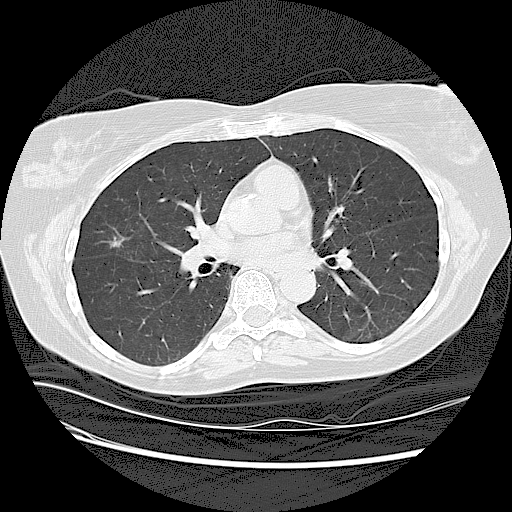
Low-dose screening chest CT, axial slice; first (baseline) screen; lung window (W 1500 / L -600 HU); slice 64 of 125 in the series. Female, age 63 years at enrolment. Current smoker at enrolment.
Lesion marked by an expert reader, bounding box <94,224,144,267> (left, top, right, bottom; pixels). Screening reader's record for this exam (one nodule recorded; not confirmed to be the boxed lesion): non-calcified nodule or mass ≥4 mm, right upper lobe, 7 × 7 mm, spiculated (stellate) margins, soft tissue attenuation. Official screen result: positive, change unspecified: nodule(s) >= 4 mm or enlarging nodule(s), mass(es), or other non-specific abnormalities suspicious for lung cancer. Participant outcome: lung cancer diagnosed 69 days after this screen — adenocarcinoma, NOS, right upper lobe, well differentiated (G1), stage IA (AJCC 6th edition), 90 mm at pathology.